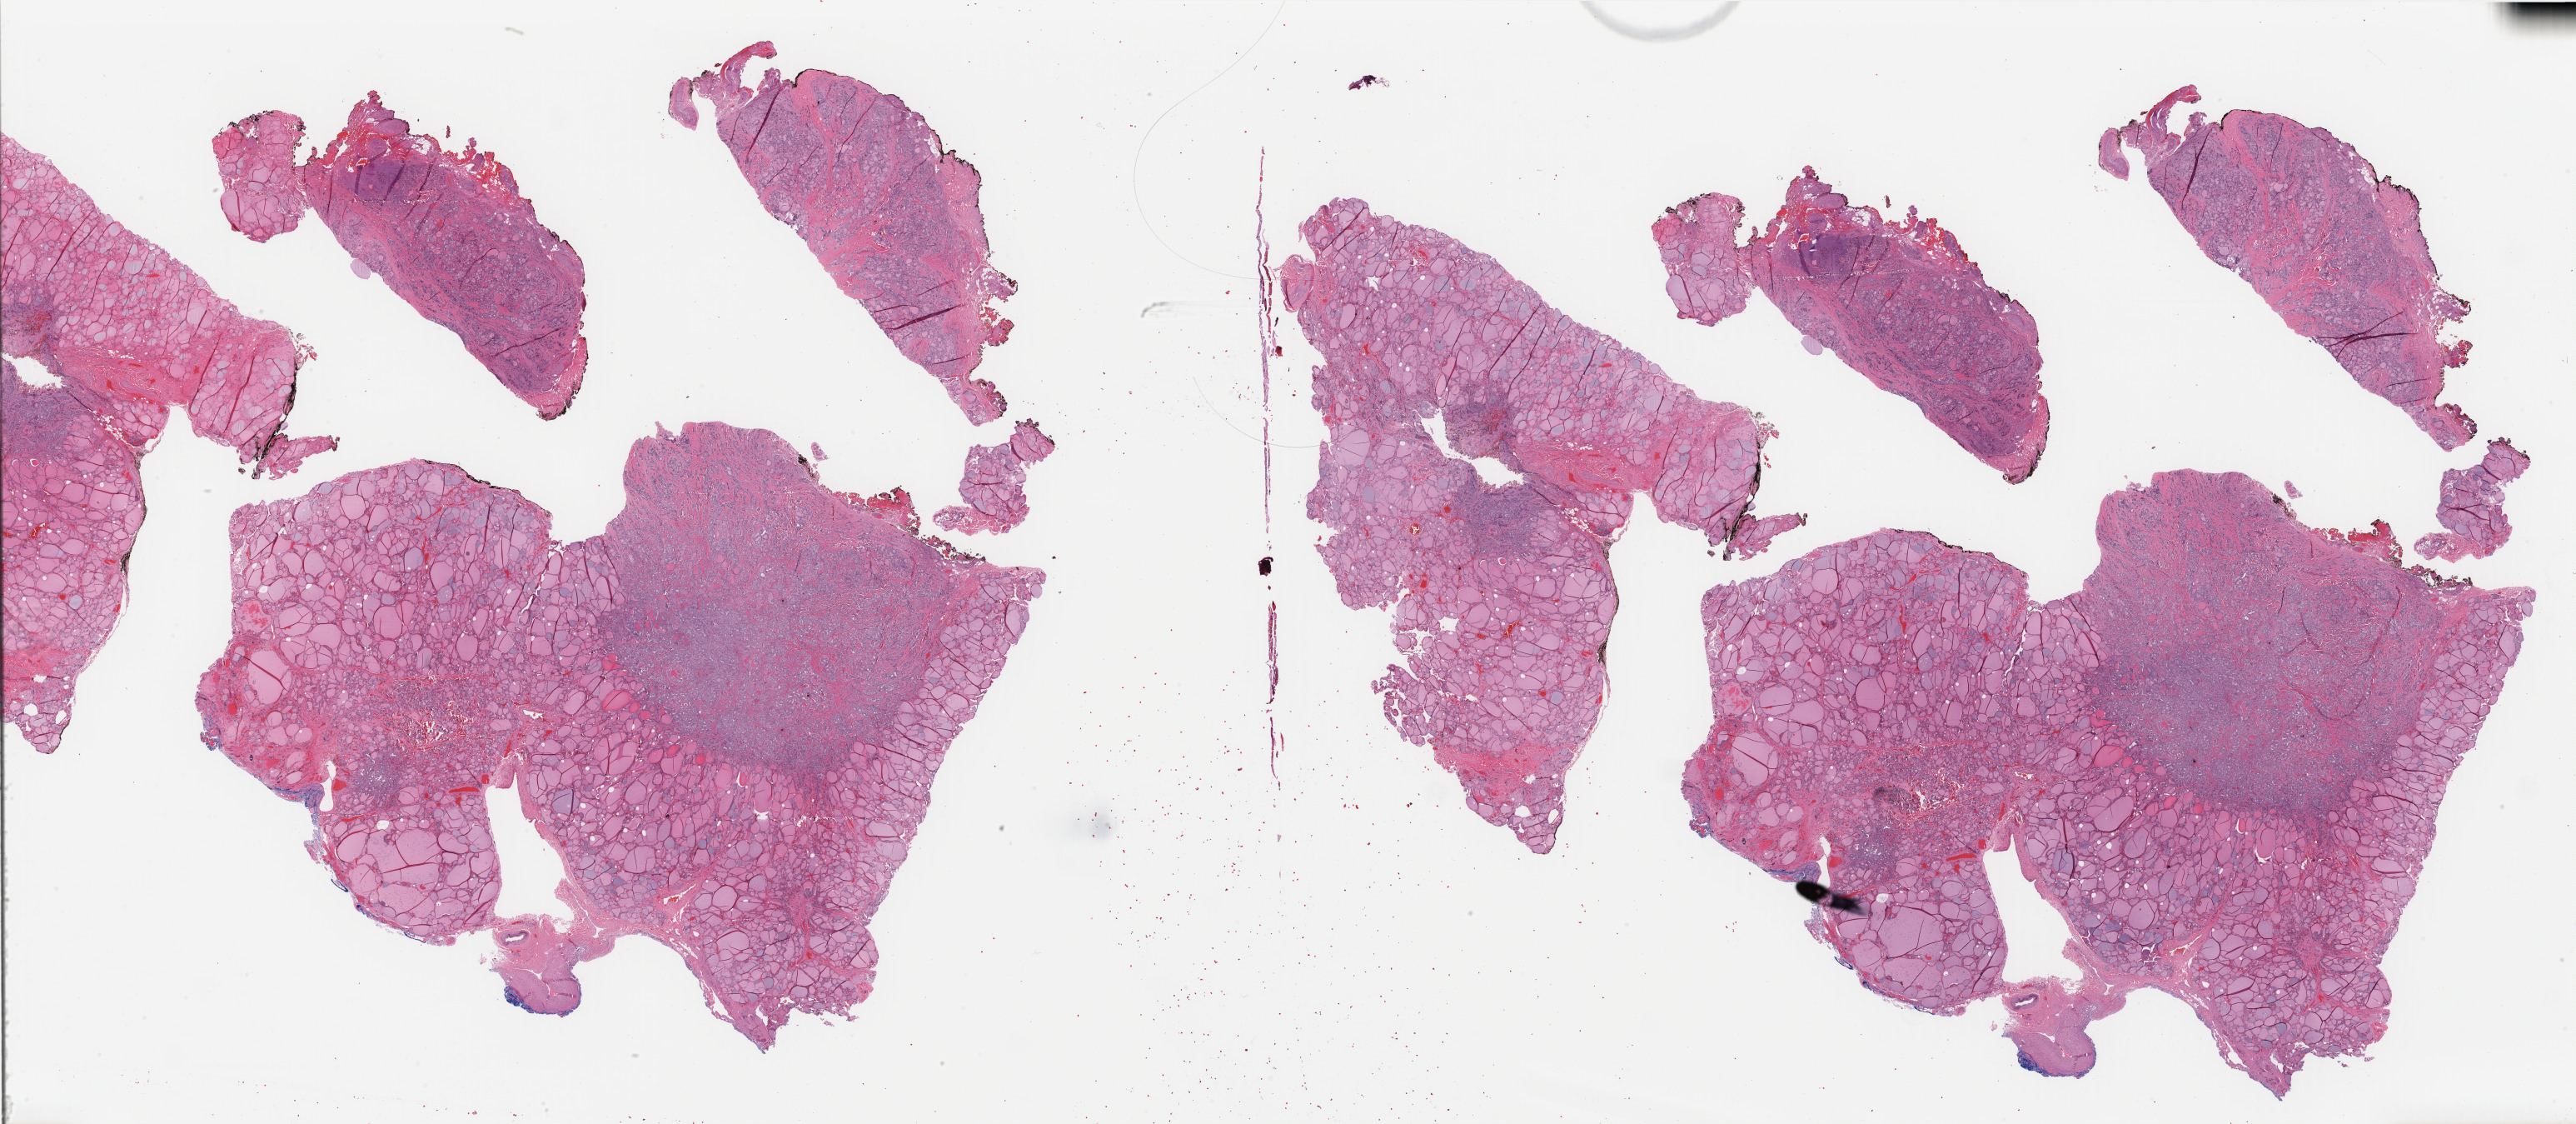
Whole-slide histology image, Hematoxylin and eosin (H&E) stained — whole scanned area (about 49.1 x 21.4 mm, slide scanned at 40x) shown as a low-resolution overview. Formalin-fixed paraffin-embedded (FFPE) diagnostic section. Sample: primary tumour, thyroid. Female patient; age at initial diagnosis 56 years.
Lymph nodes positive (case pathology): 0 of 1 examined. TNM: T3 N0 M0. Laterality: bilateral. AJCC pathologic stage: III (7th edition). Diagnosis: Papillary carcinoma, follicular variant (thyroid gland).